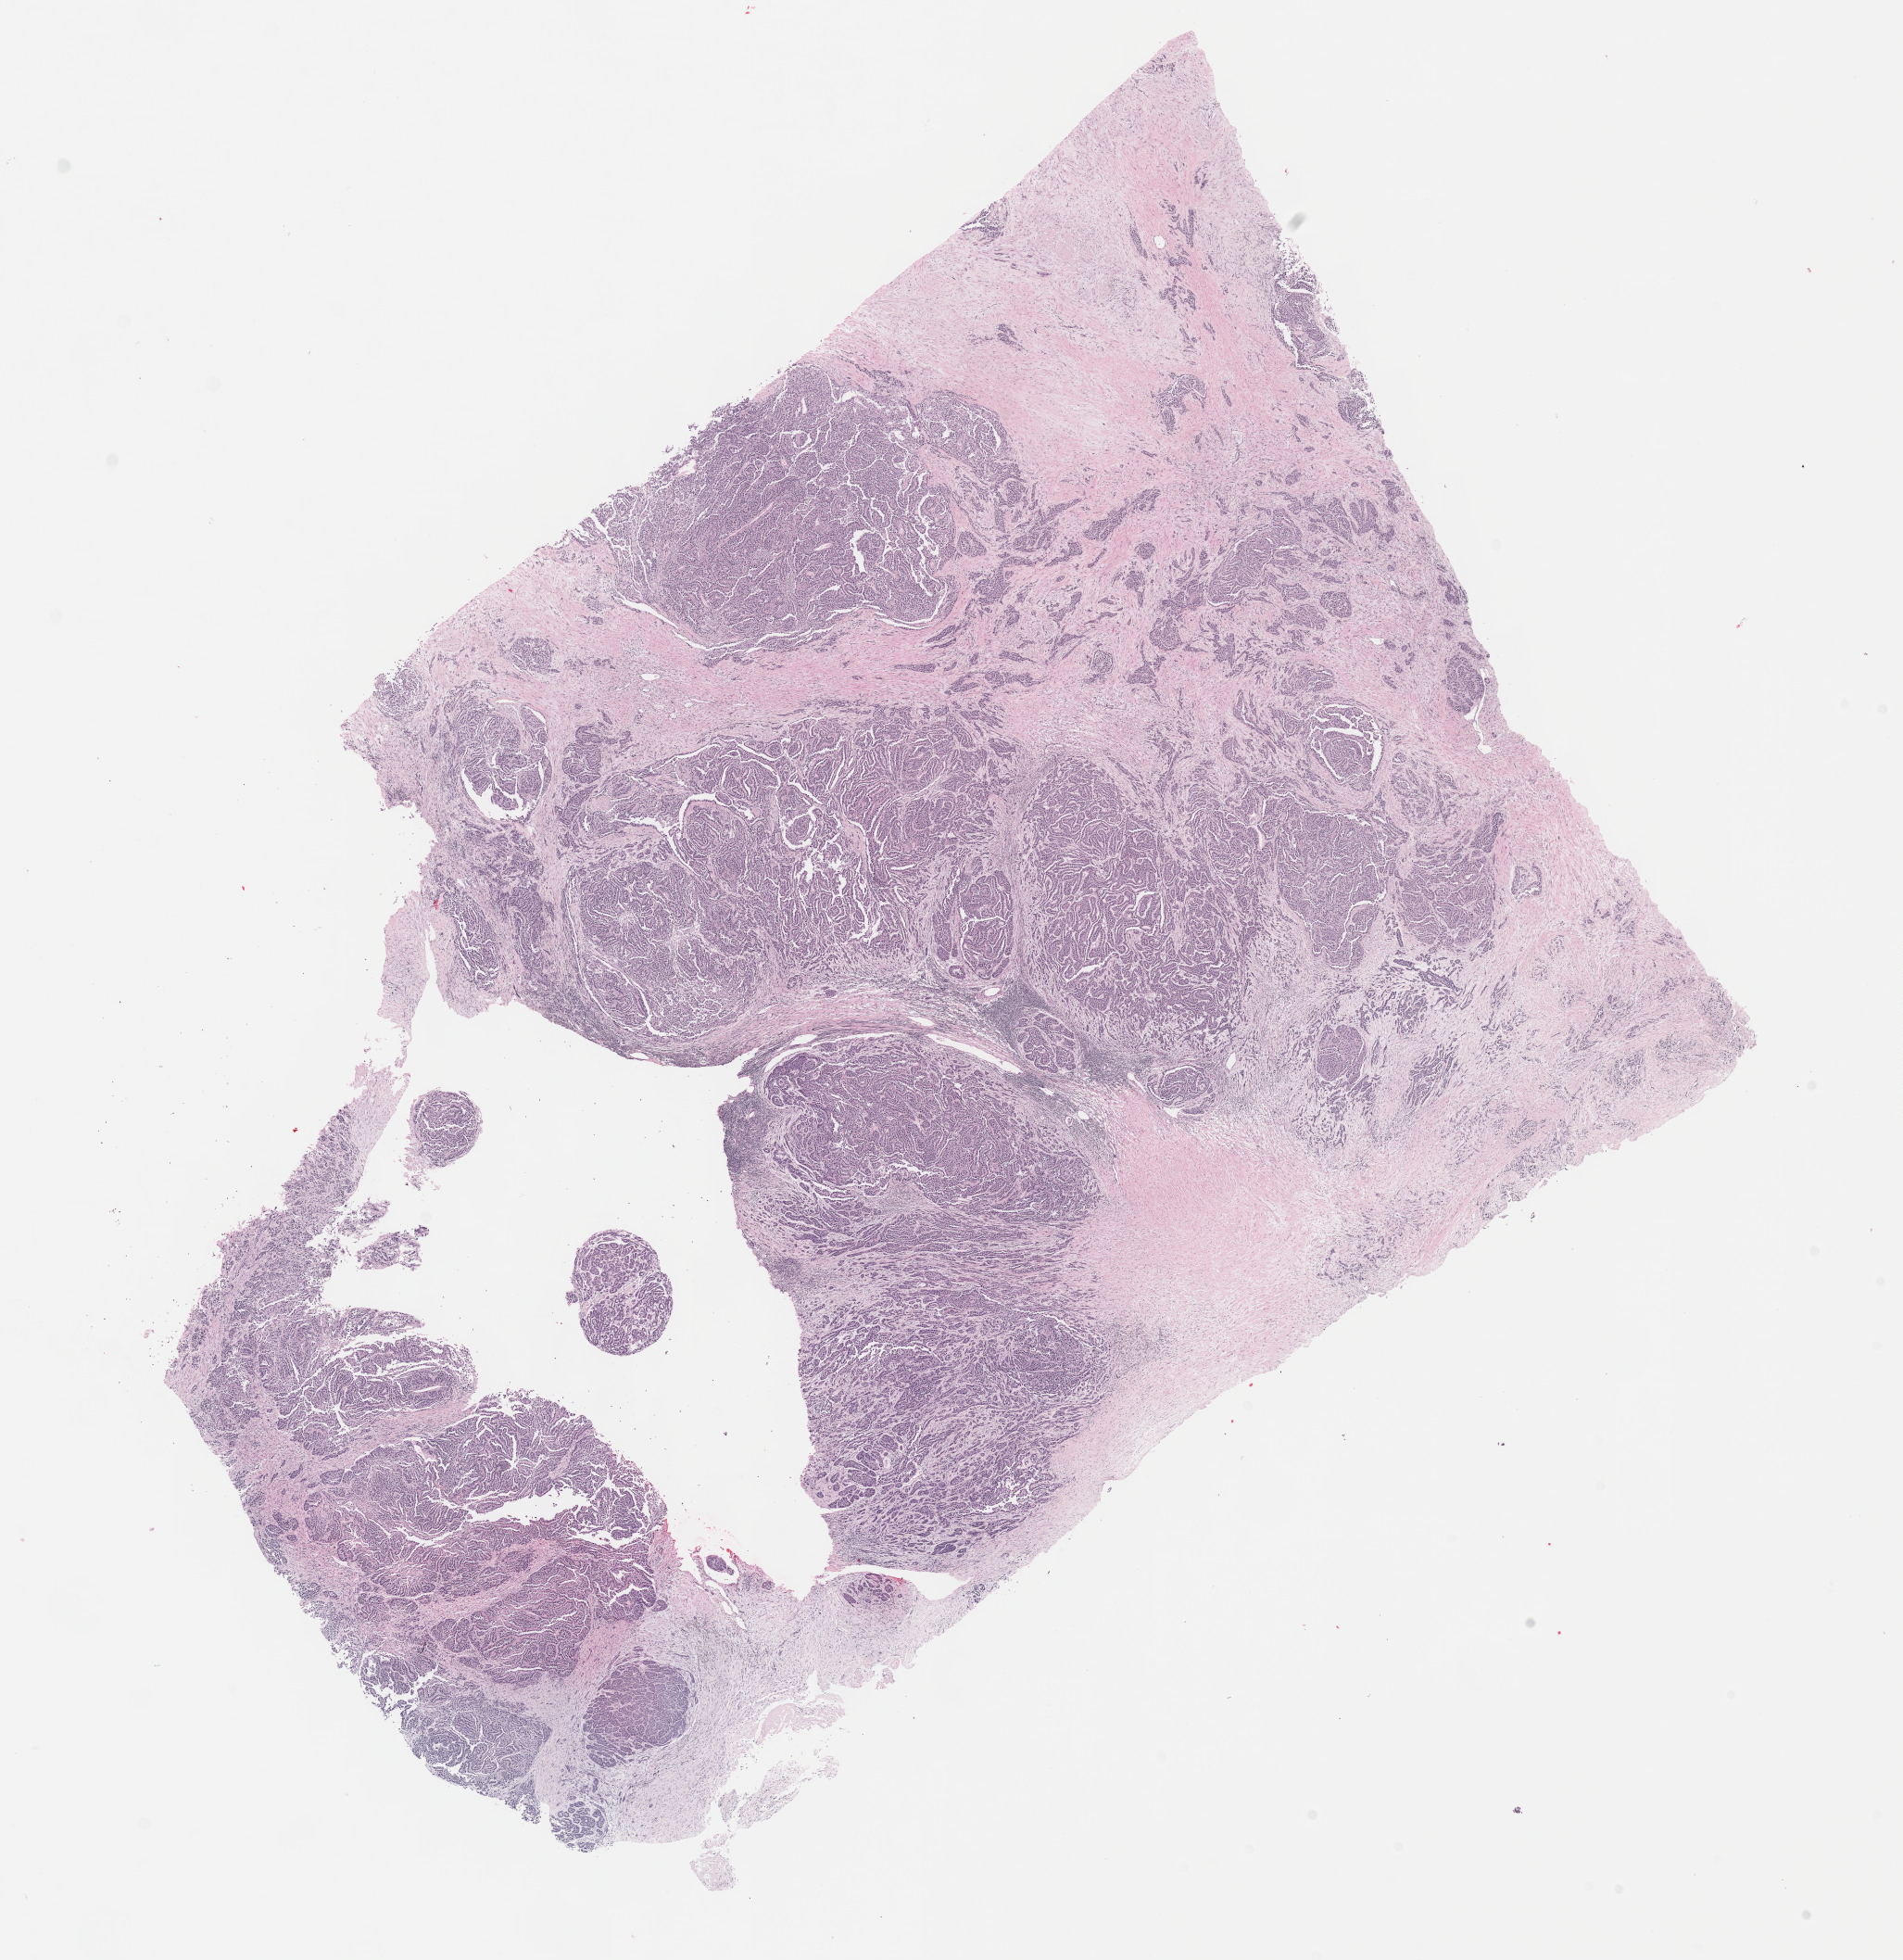
Whole-slide histology image, H&E-stained, shown as a low-resolution overview of the whole scanned area (about 16.6 x 17.1 mm, slide scanned at 40x). FFPE section. Primary tumour sample from the kidney. Male, age 41 years at initial diagnosis.
AJCC pathologic stage: IV (6th edition). Laterality: right. Pathologic diagnosis: Papillary adenocarcinoma, NOS.